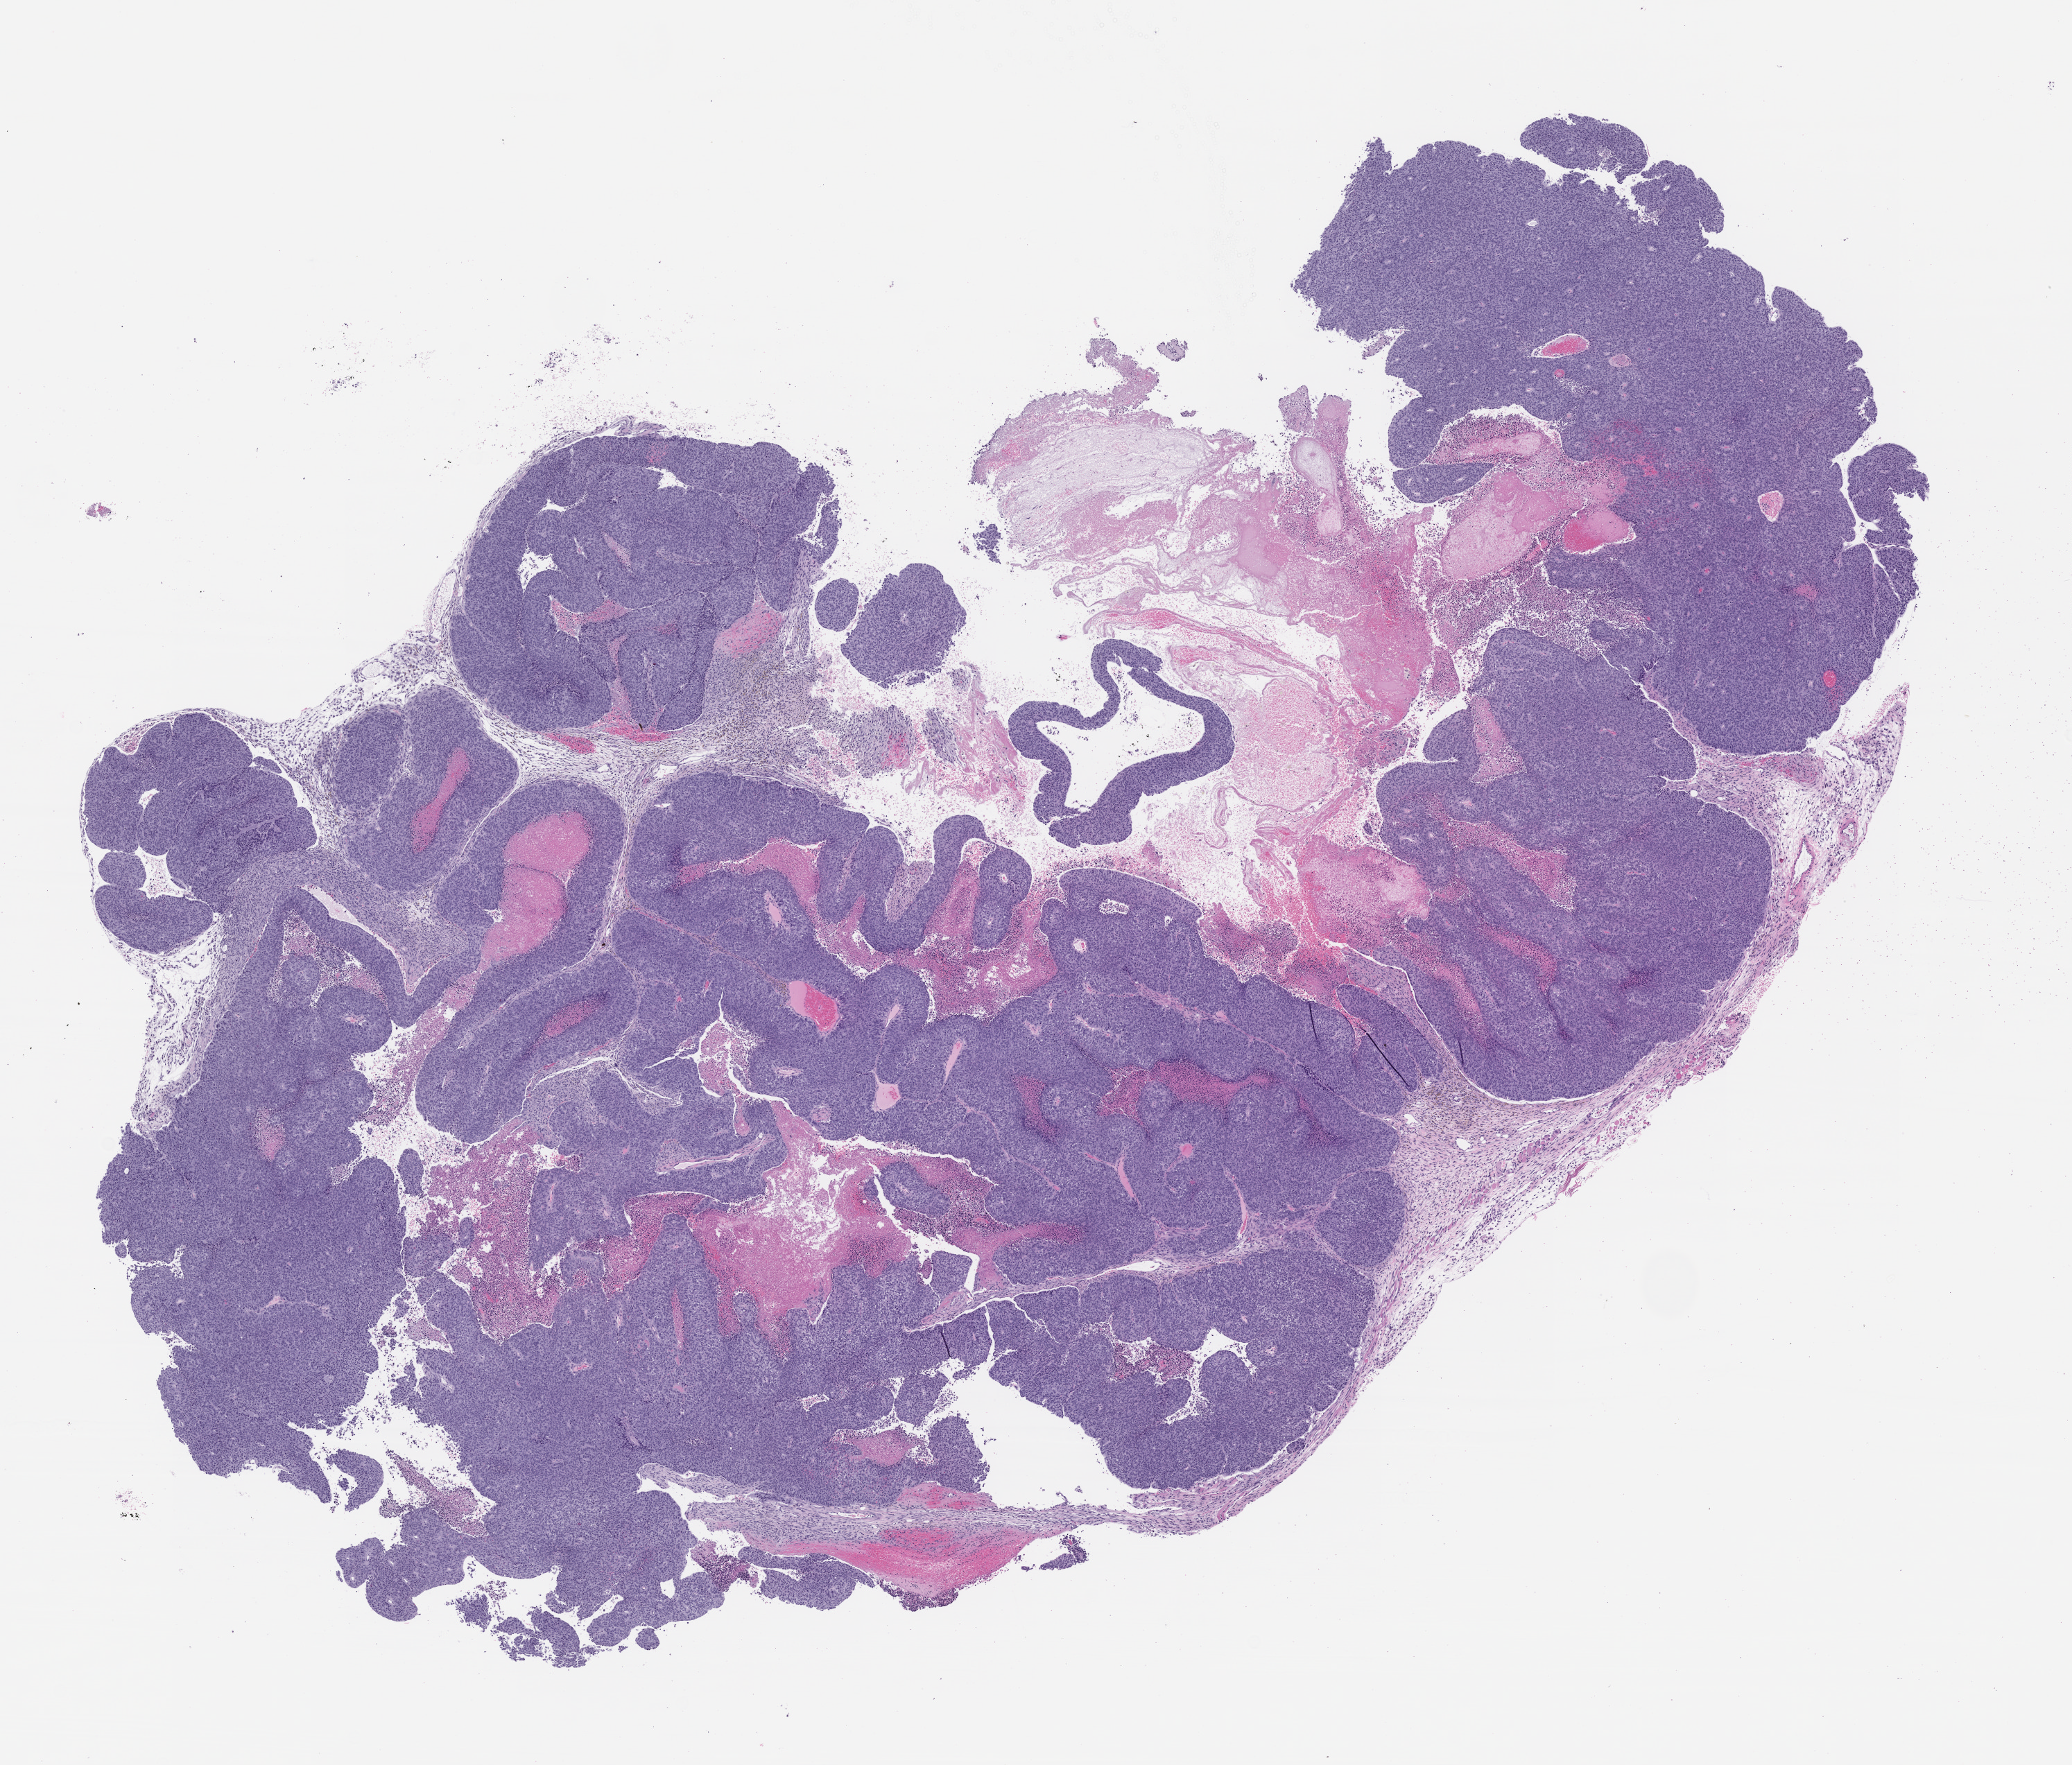
Hematoxylin and eosin (H&E) whole-slide image of a patient-derived xenograft (PDX) tumor grown in a mouse, passage 0 — low-resolution overview of the scanned area, about 12.0 x 10.2 mm, FFPE section, originating tumor site category: vagina.
Originating patient diagnosis: Vaginal Carcinoma.